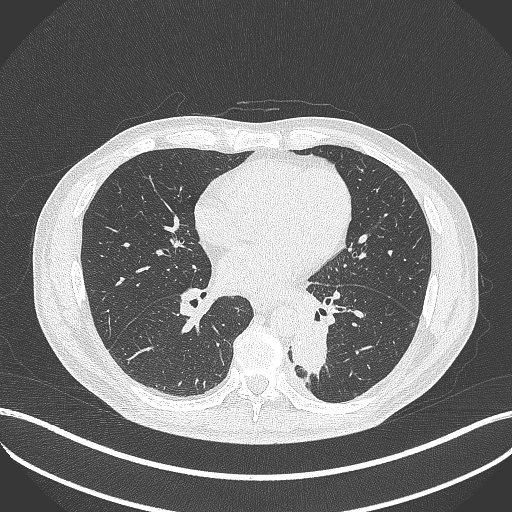
Chest CT, one axial slice. Position 182 of 451 along the scan axis. Lung window (W 1500 / L -600 HU). 512 × 512 image matrix, field of view 400 × 400 mm. Patient: male, 72 years. From the clinical record (not read from this slice): clinical TNM (as recorded): T2b N0 M1.
Annotated regions visible in this slice (bounding box drawn by a radiologist):
- lung tumour (recorded histology: adenocarcinoma): bounding box <290,318,333,379> (left, top, right, bottom; pixels)